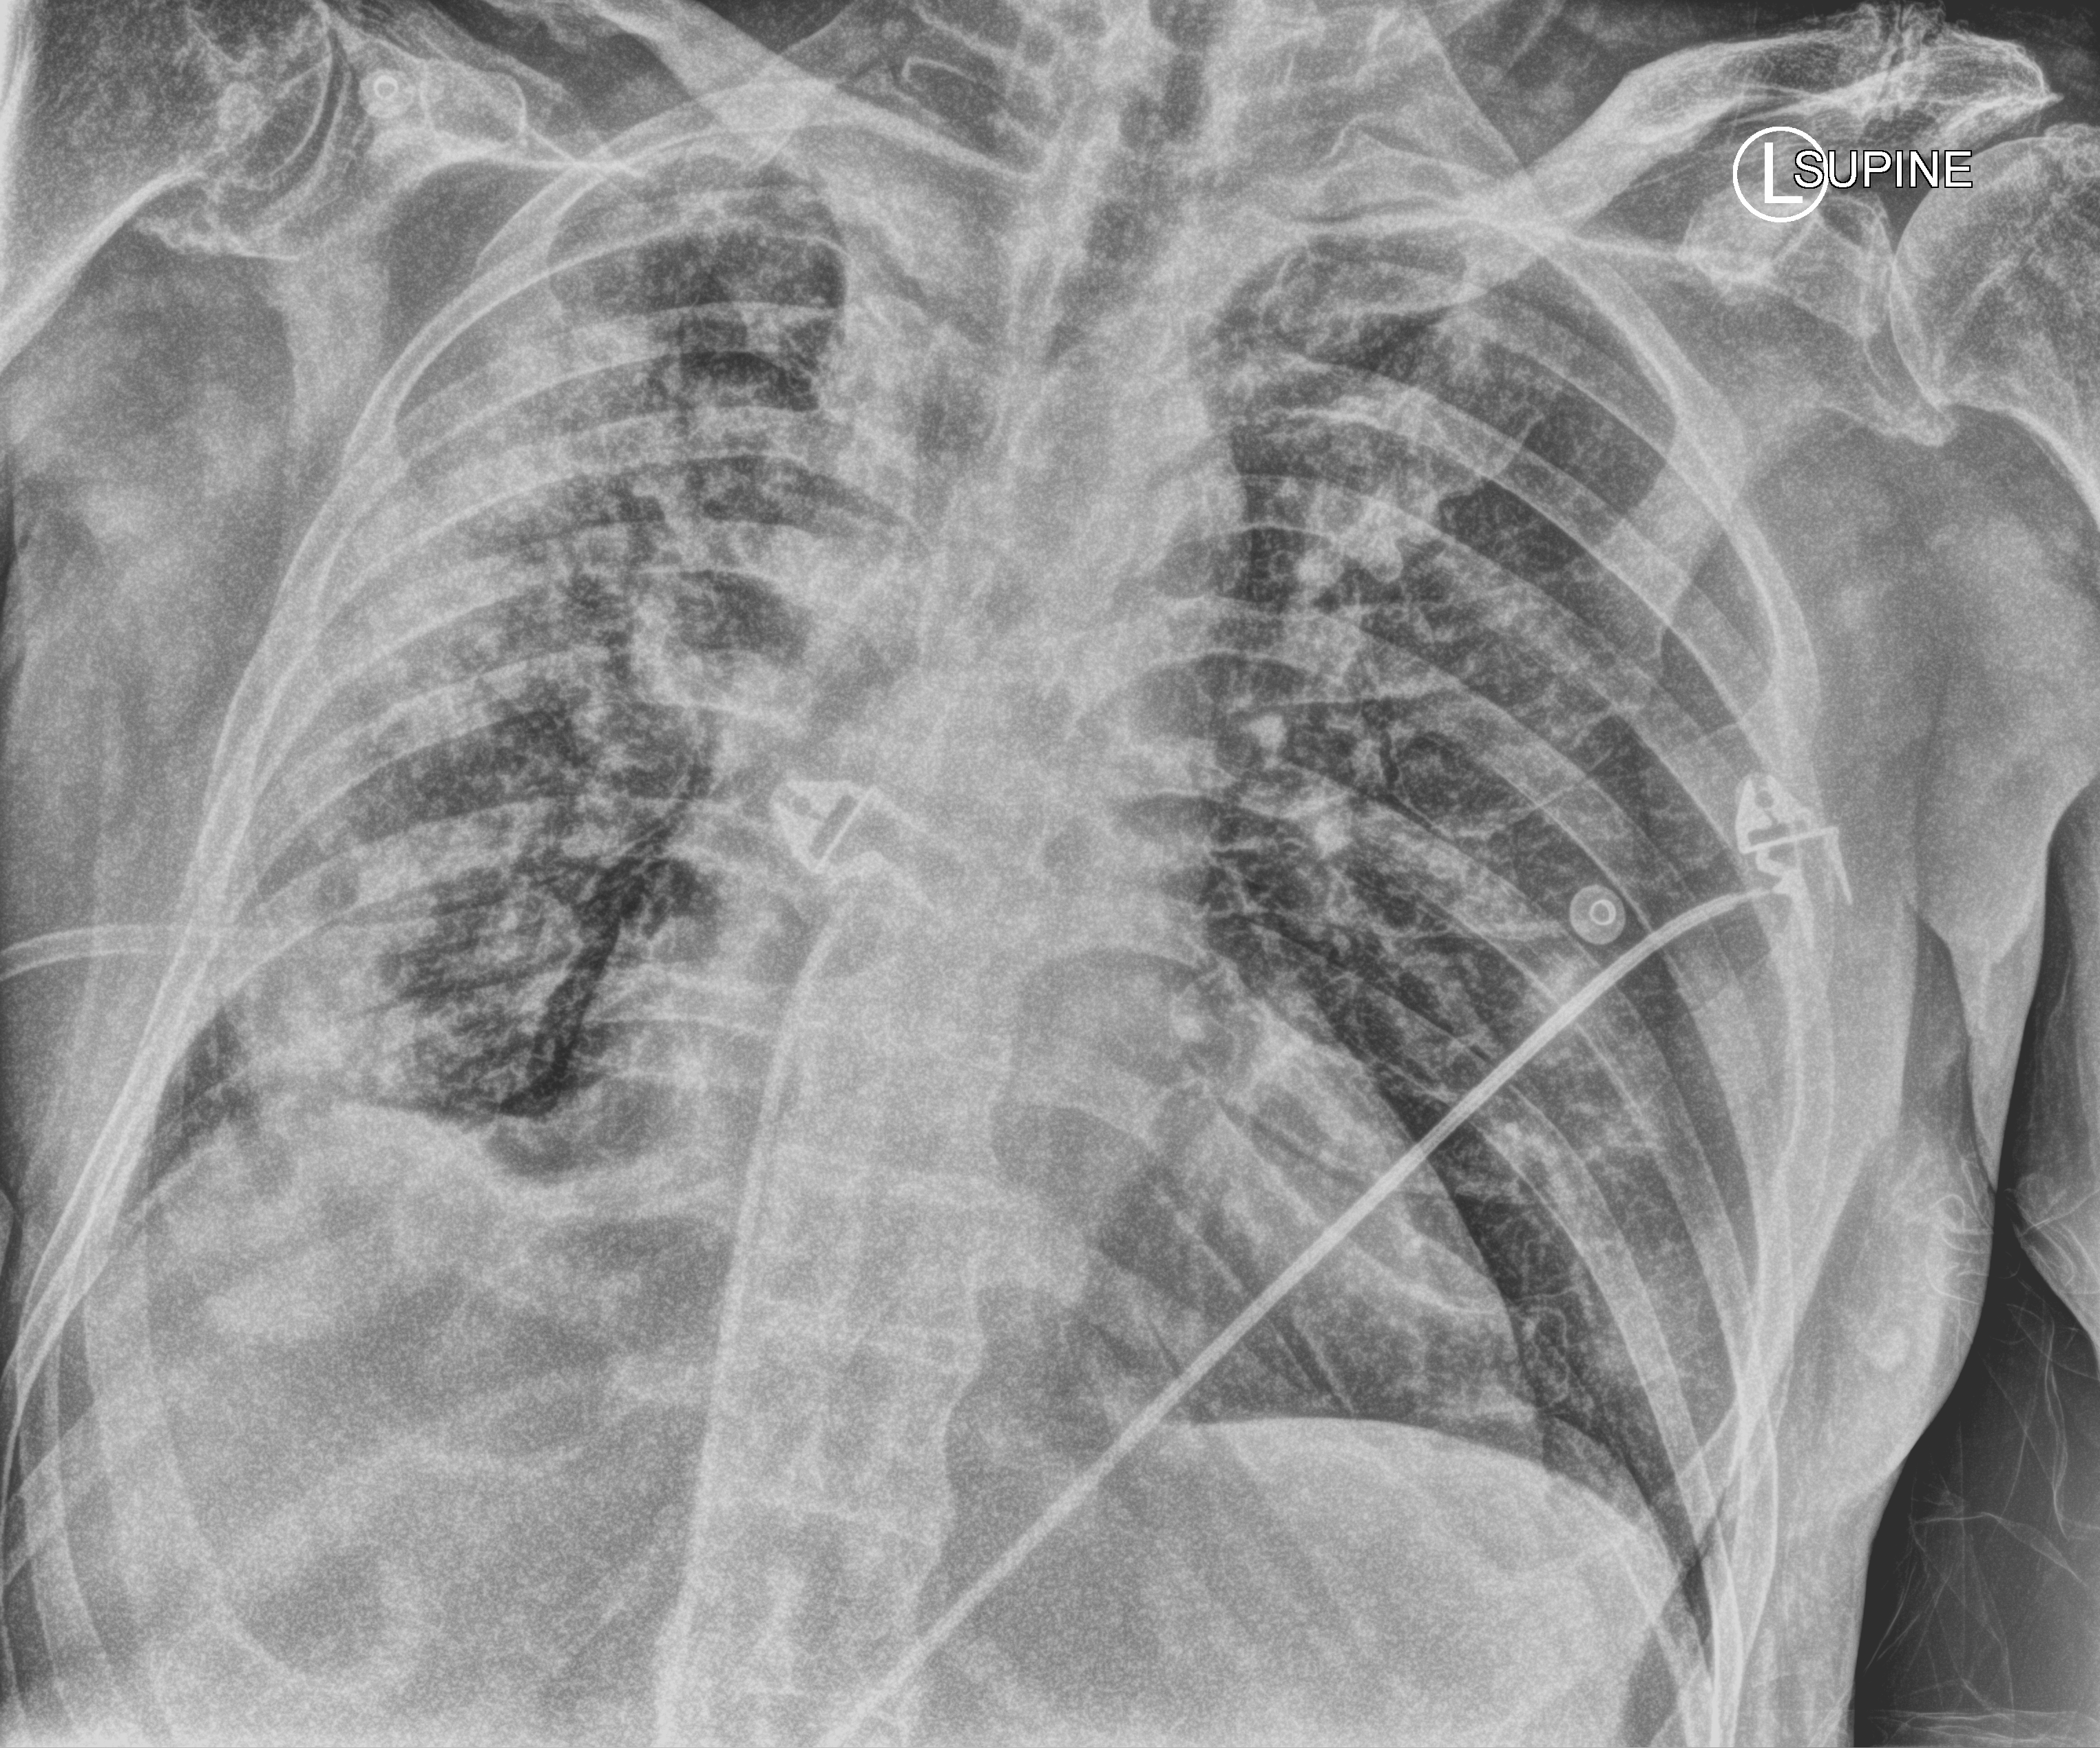
Bedside chest radiograph (computed radiography); anteroposterior (AP) projection. Patient hospitalised with COVID-19; male, aged 75–90 years.
Hospital-stay facts (about this admission, not read from this image; timing relative to this image not recorded): mechanically ventilated during this hospital stay: no; admitted to intensive care during this hospital stay: no; hypertension (admission record): yes.